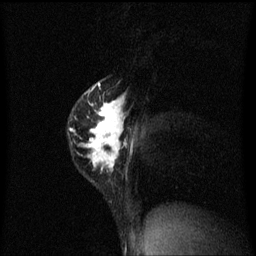
Breast MRI (dynamic contrast-enhanced), one sagittal slice. Position 43 of 60 along the scan axis. Dynamic contrast-enhanced series, image 2 of 3 at this slice position (ordered by acquisition). 1.5 T. TE 4.2 ms, TR 8.4 ms. 2 mm slice thickness. 256 × 256 image matrix, field of view 200 × 200 mm. Patient: female, 40 years.
Annotated regions visible in this slice (semi-automatically segmented with operator editing):
- analysis volume of interest (the breast-tissue region the enhancement analysis was run in; not a lesion): box from (x=69, y=78) to (x=128, y=185) px
- tumour enhancement mask (voxels above the 70 % enhancement threshold inside the analysis volume of interest): (x=70, y=82)–(x=127, y=171)